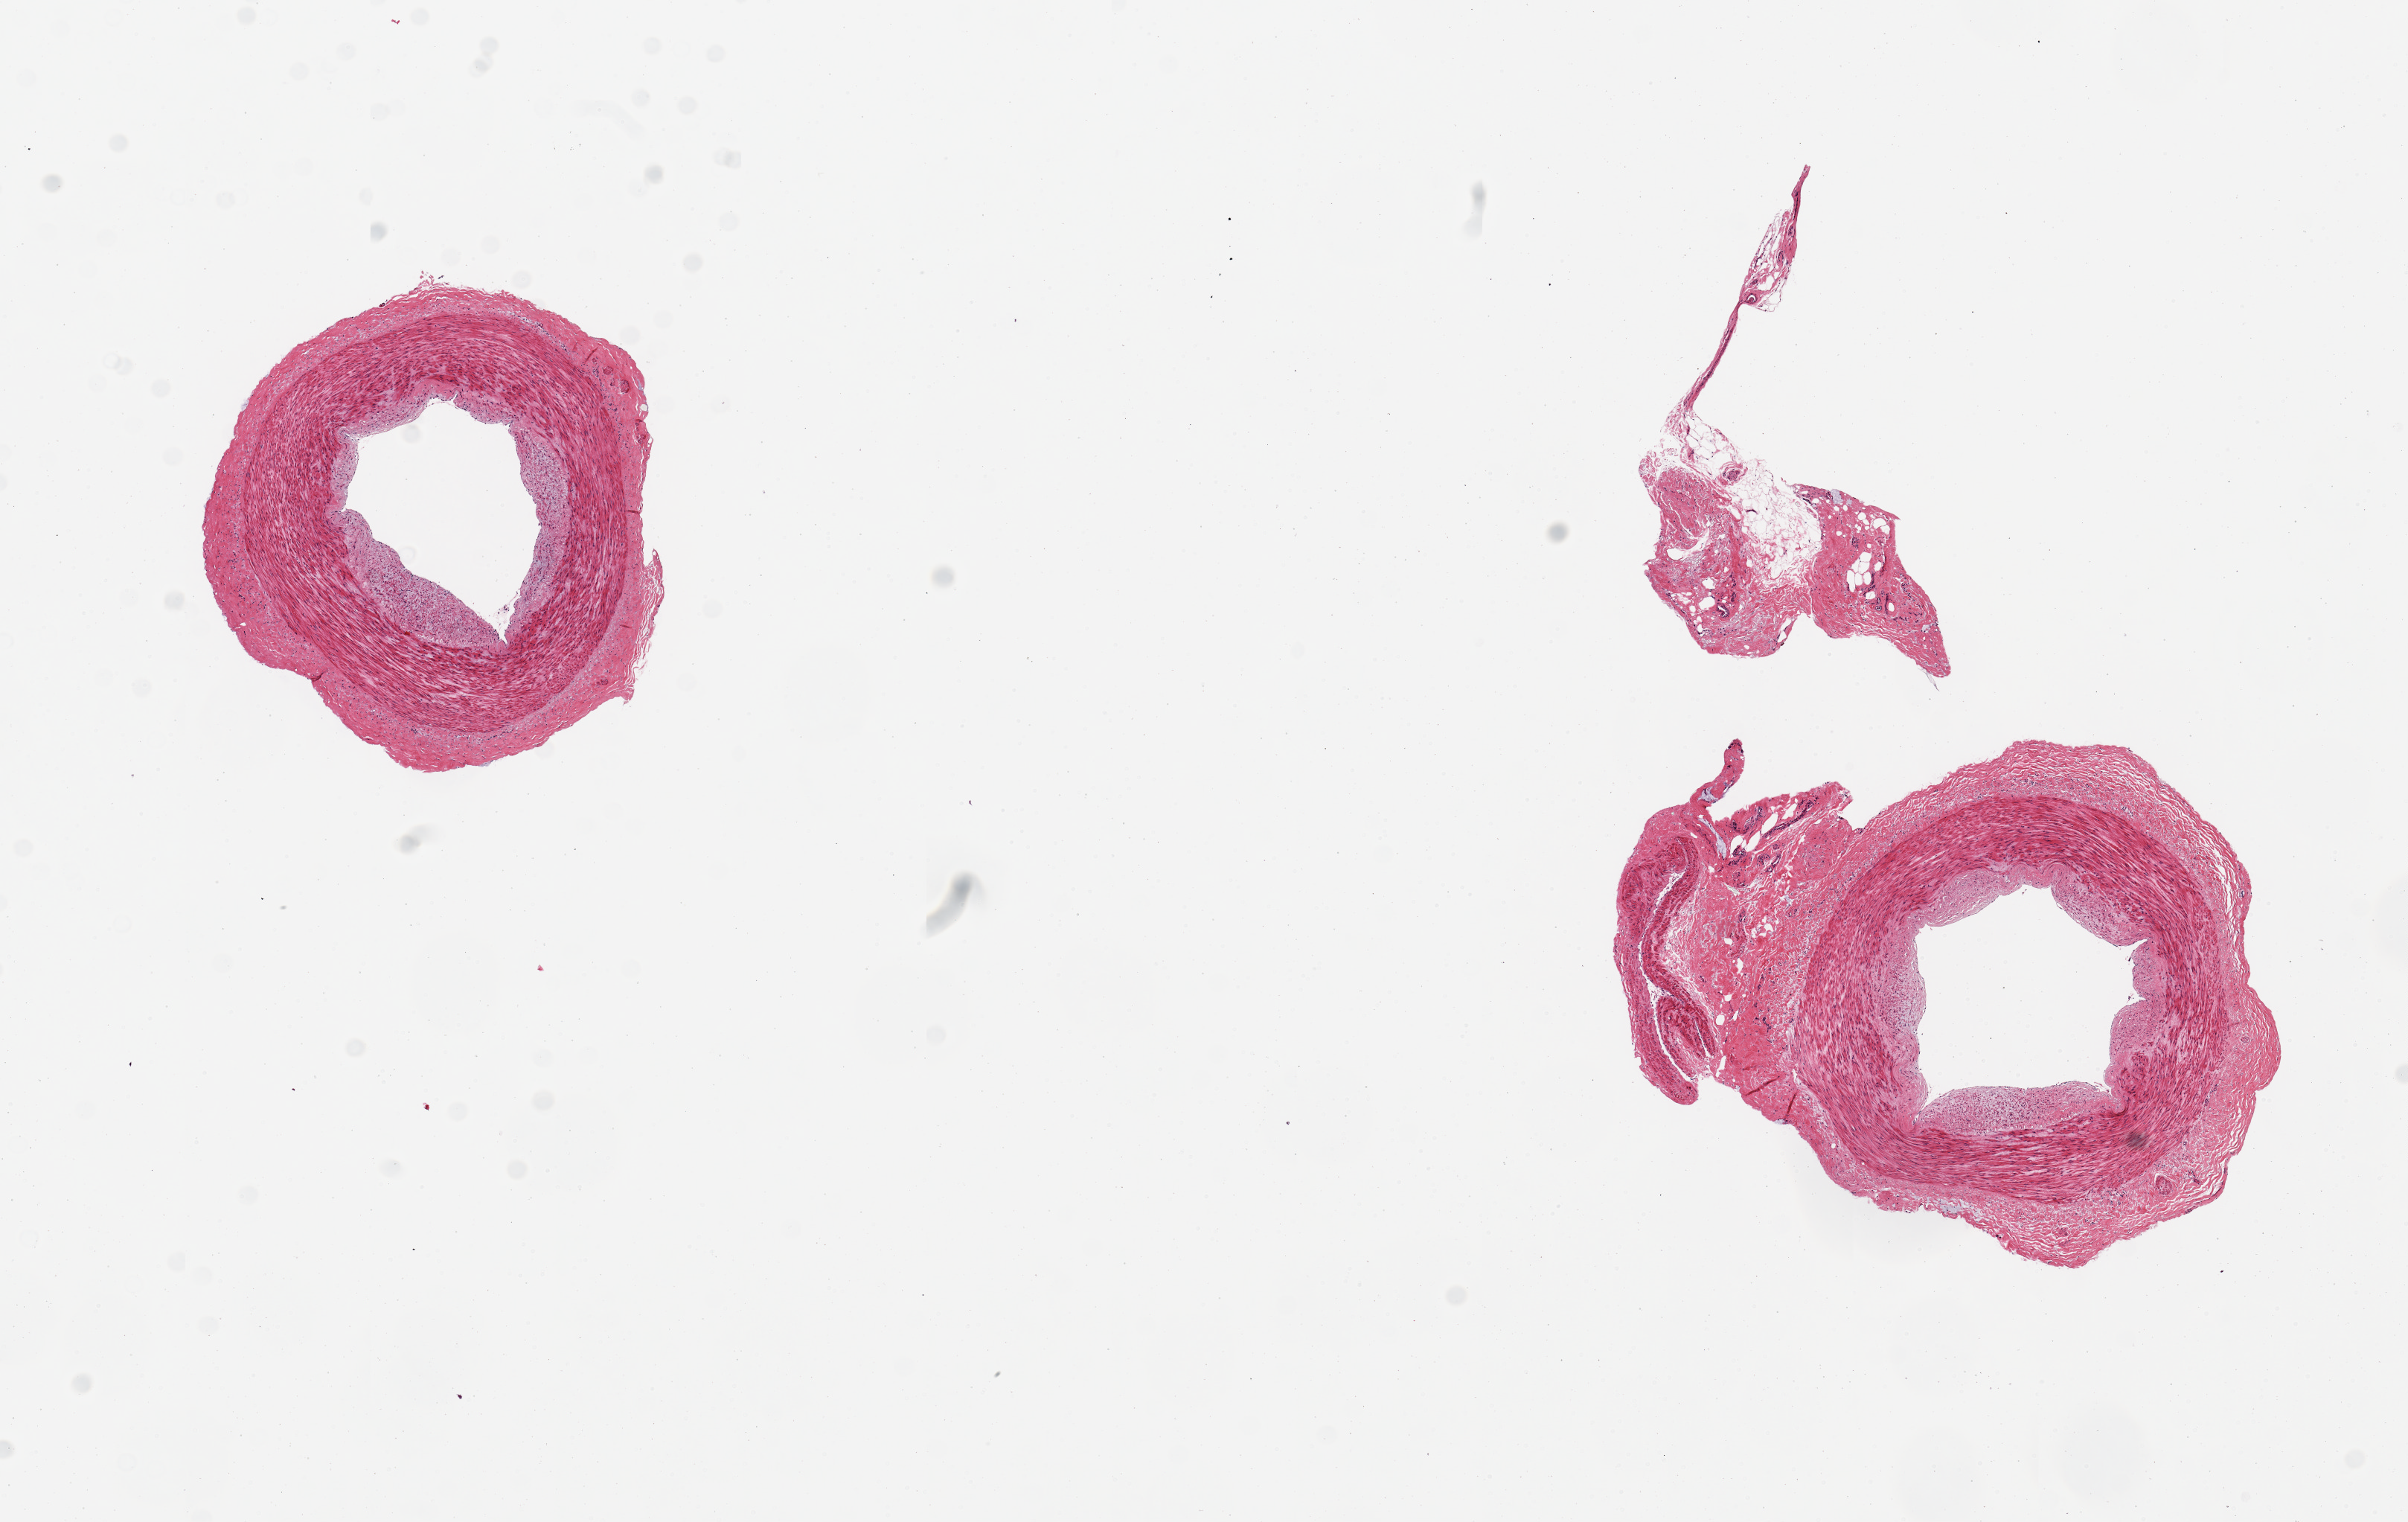
Digitized H&E-stained section, shown as a low-resolution overview of the whole scanned area (about 12.8 x 8.1 mm, from a 20x scan), PAXgene-fixed, paraffin-embedded tissue, target tissue: tibial artery, donor tissue sample. Male donor.
Reviewer comment on this tissue sample: 3 pieces; 1 represents fibrovascular and adipose tissue; vein attached to 1 artery.